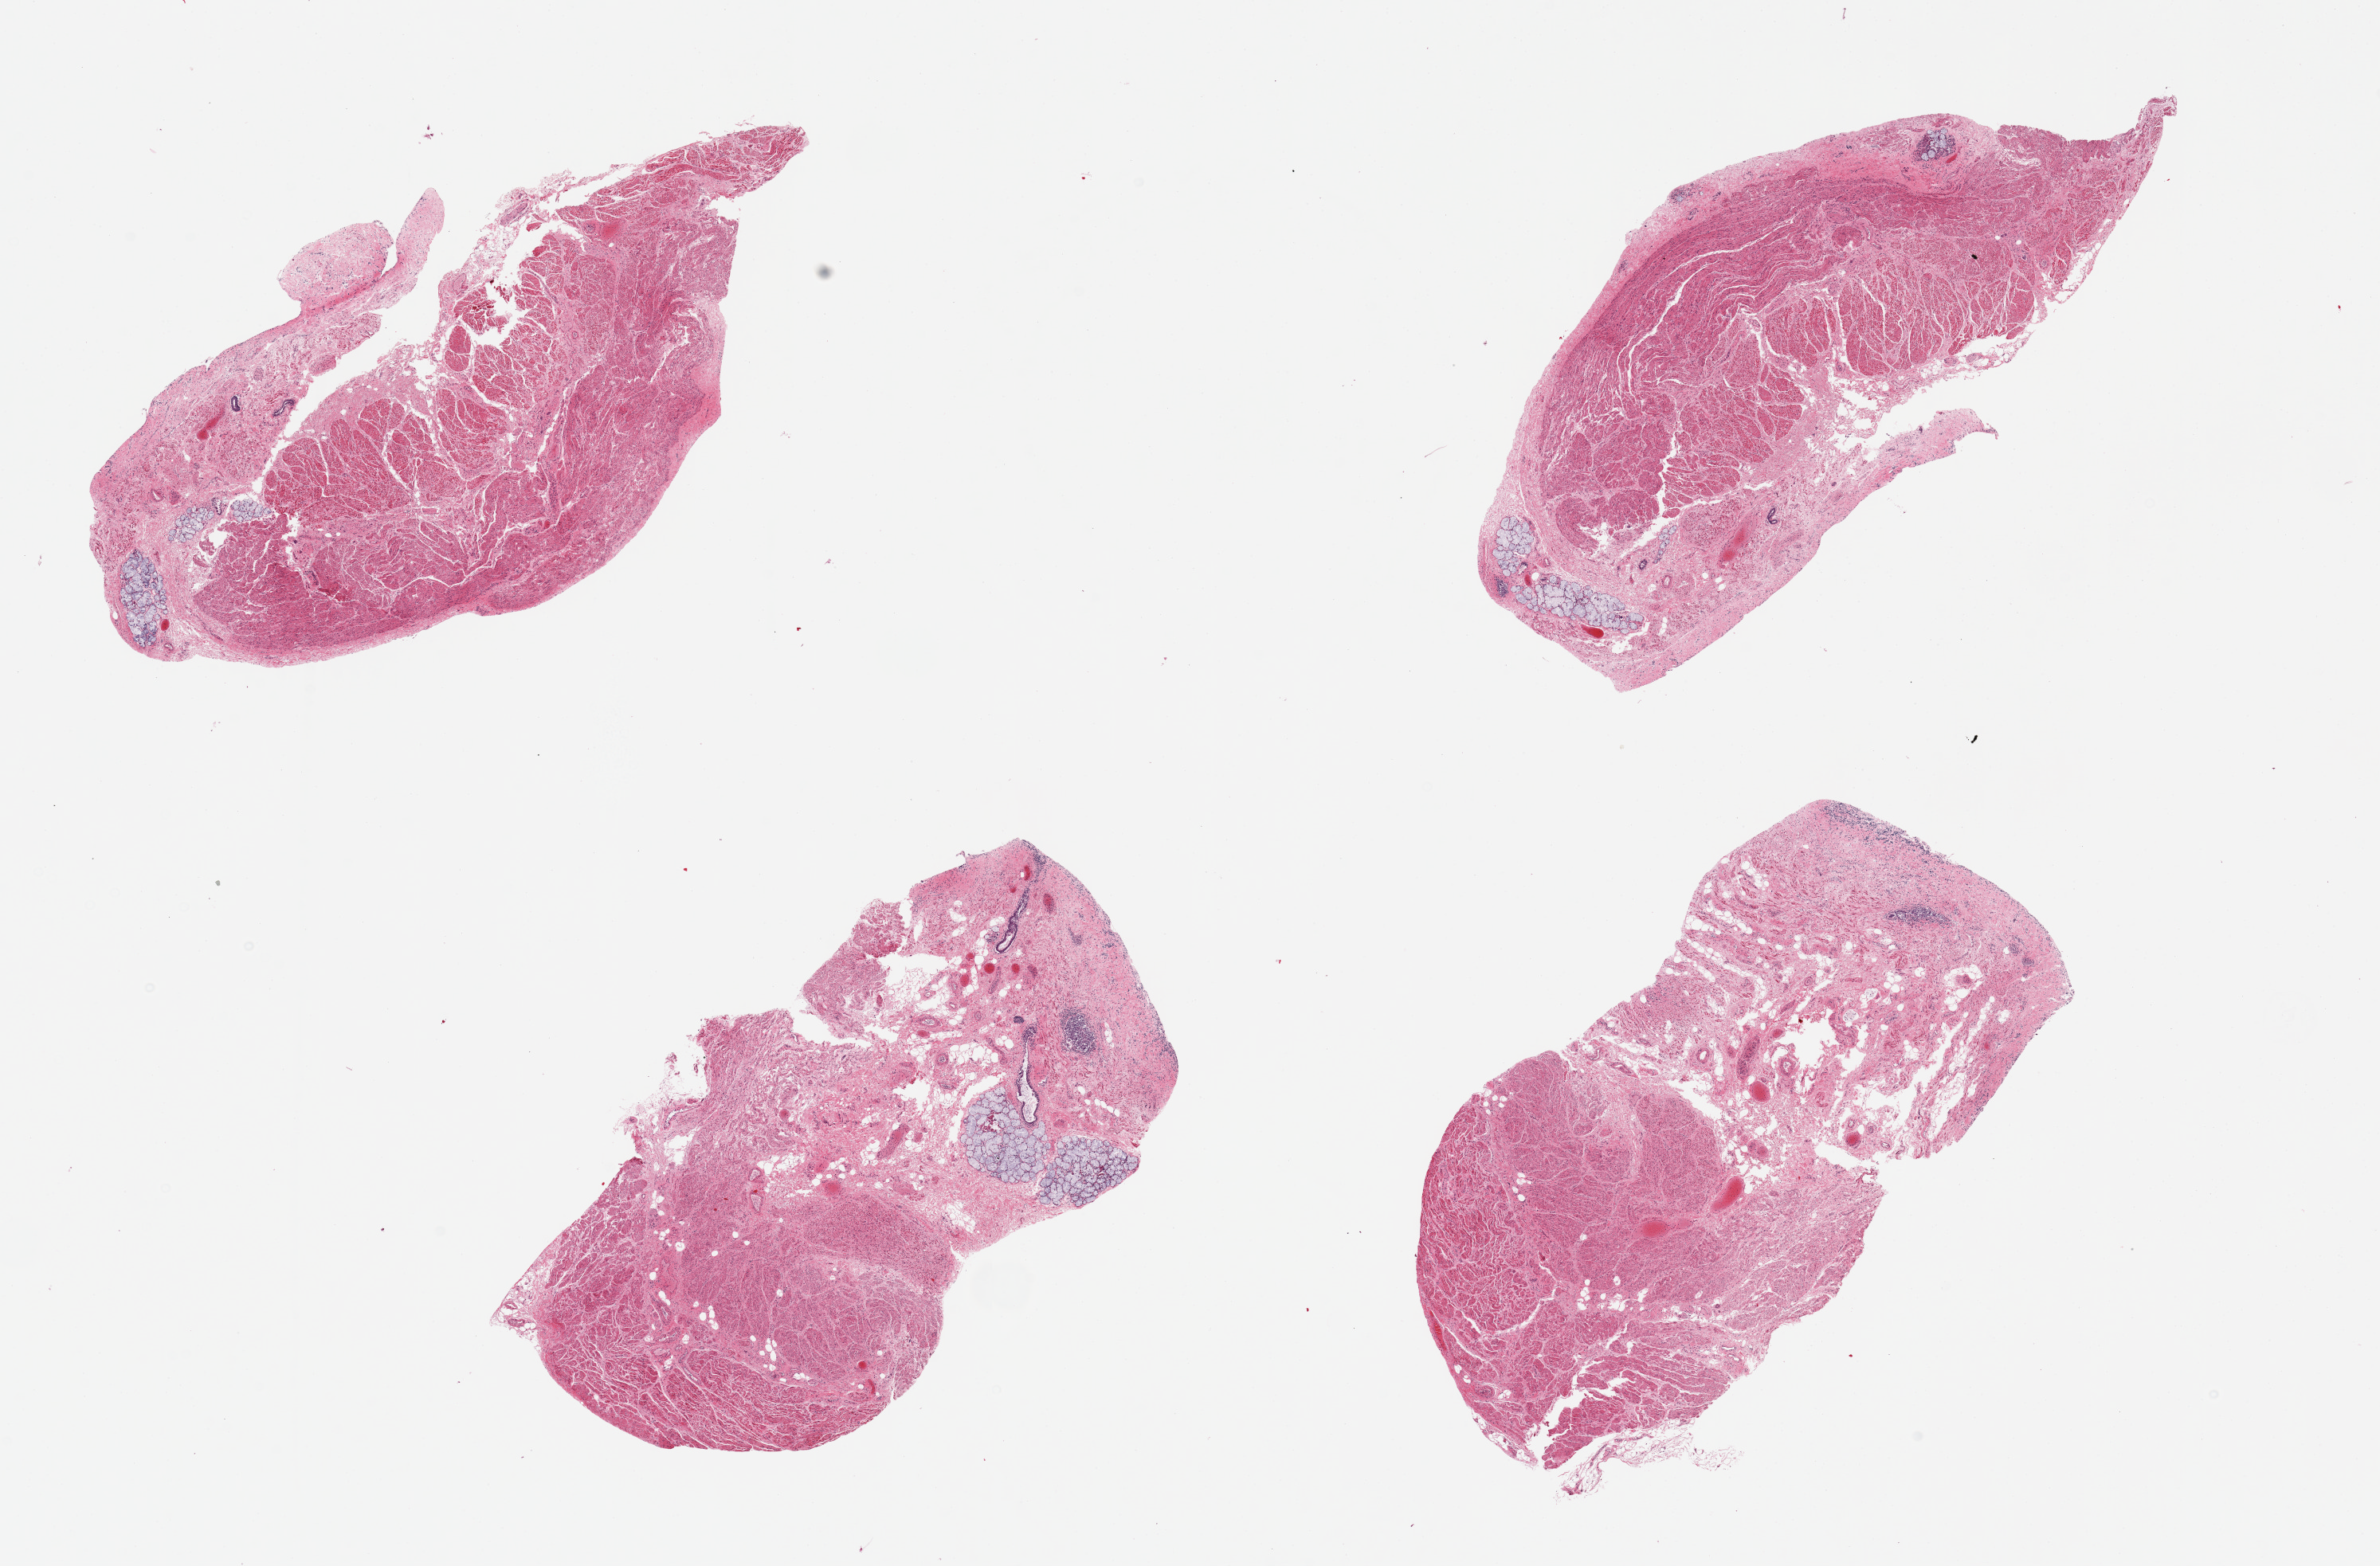
Haematoxylin and eosin whole-slide image, brightfield, a low-resolution overview of the entire scanned area, about 23.6 x 15.6 mm (acquisition: 20x scan), PAXgene-fixed paraffin-embedded (PFPE) section, section of gastroesophageal junction (target tissue), tissue donor sample. Donor sex: female.
Reviewer comment on this tissue sample: 4 pieces; muscle and submucosal glands.